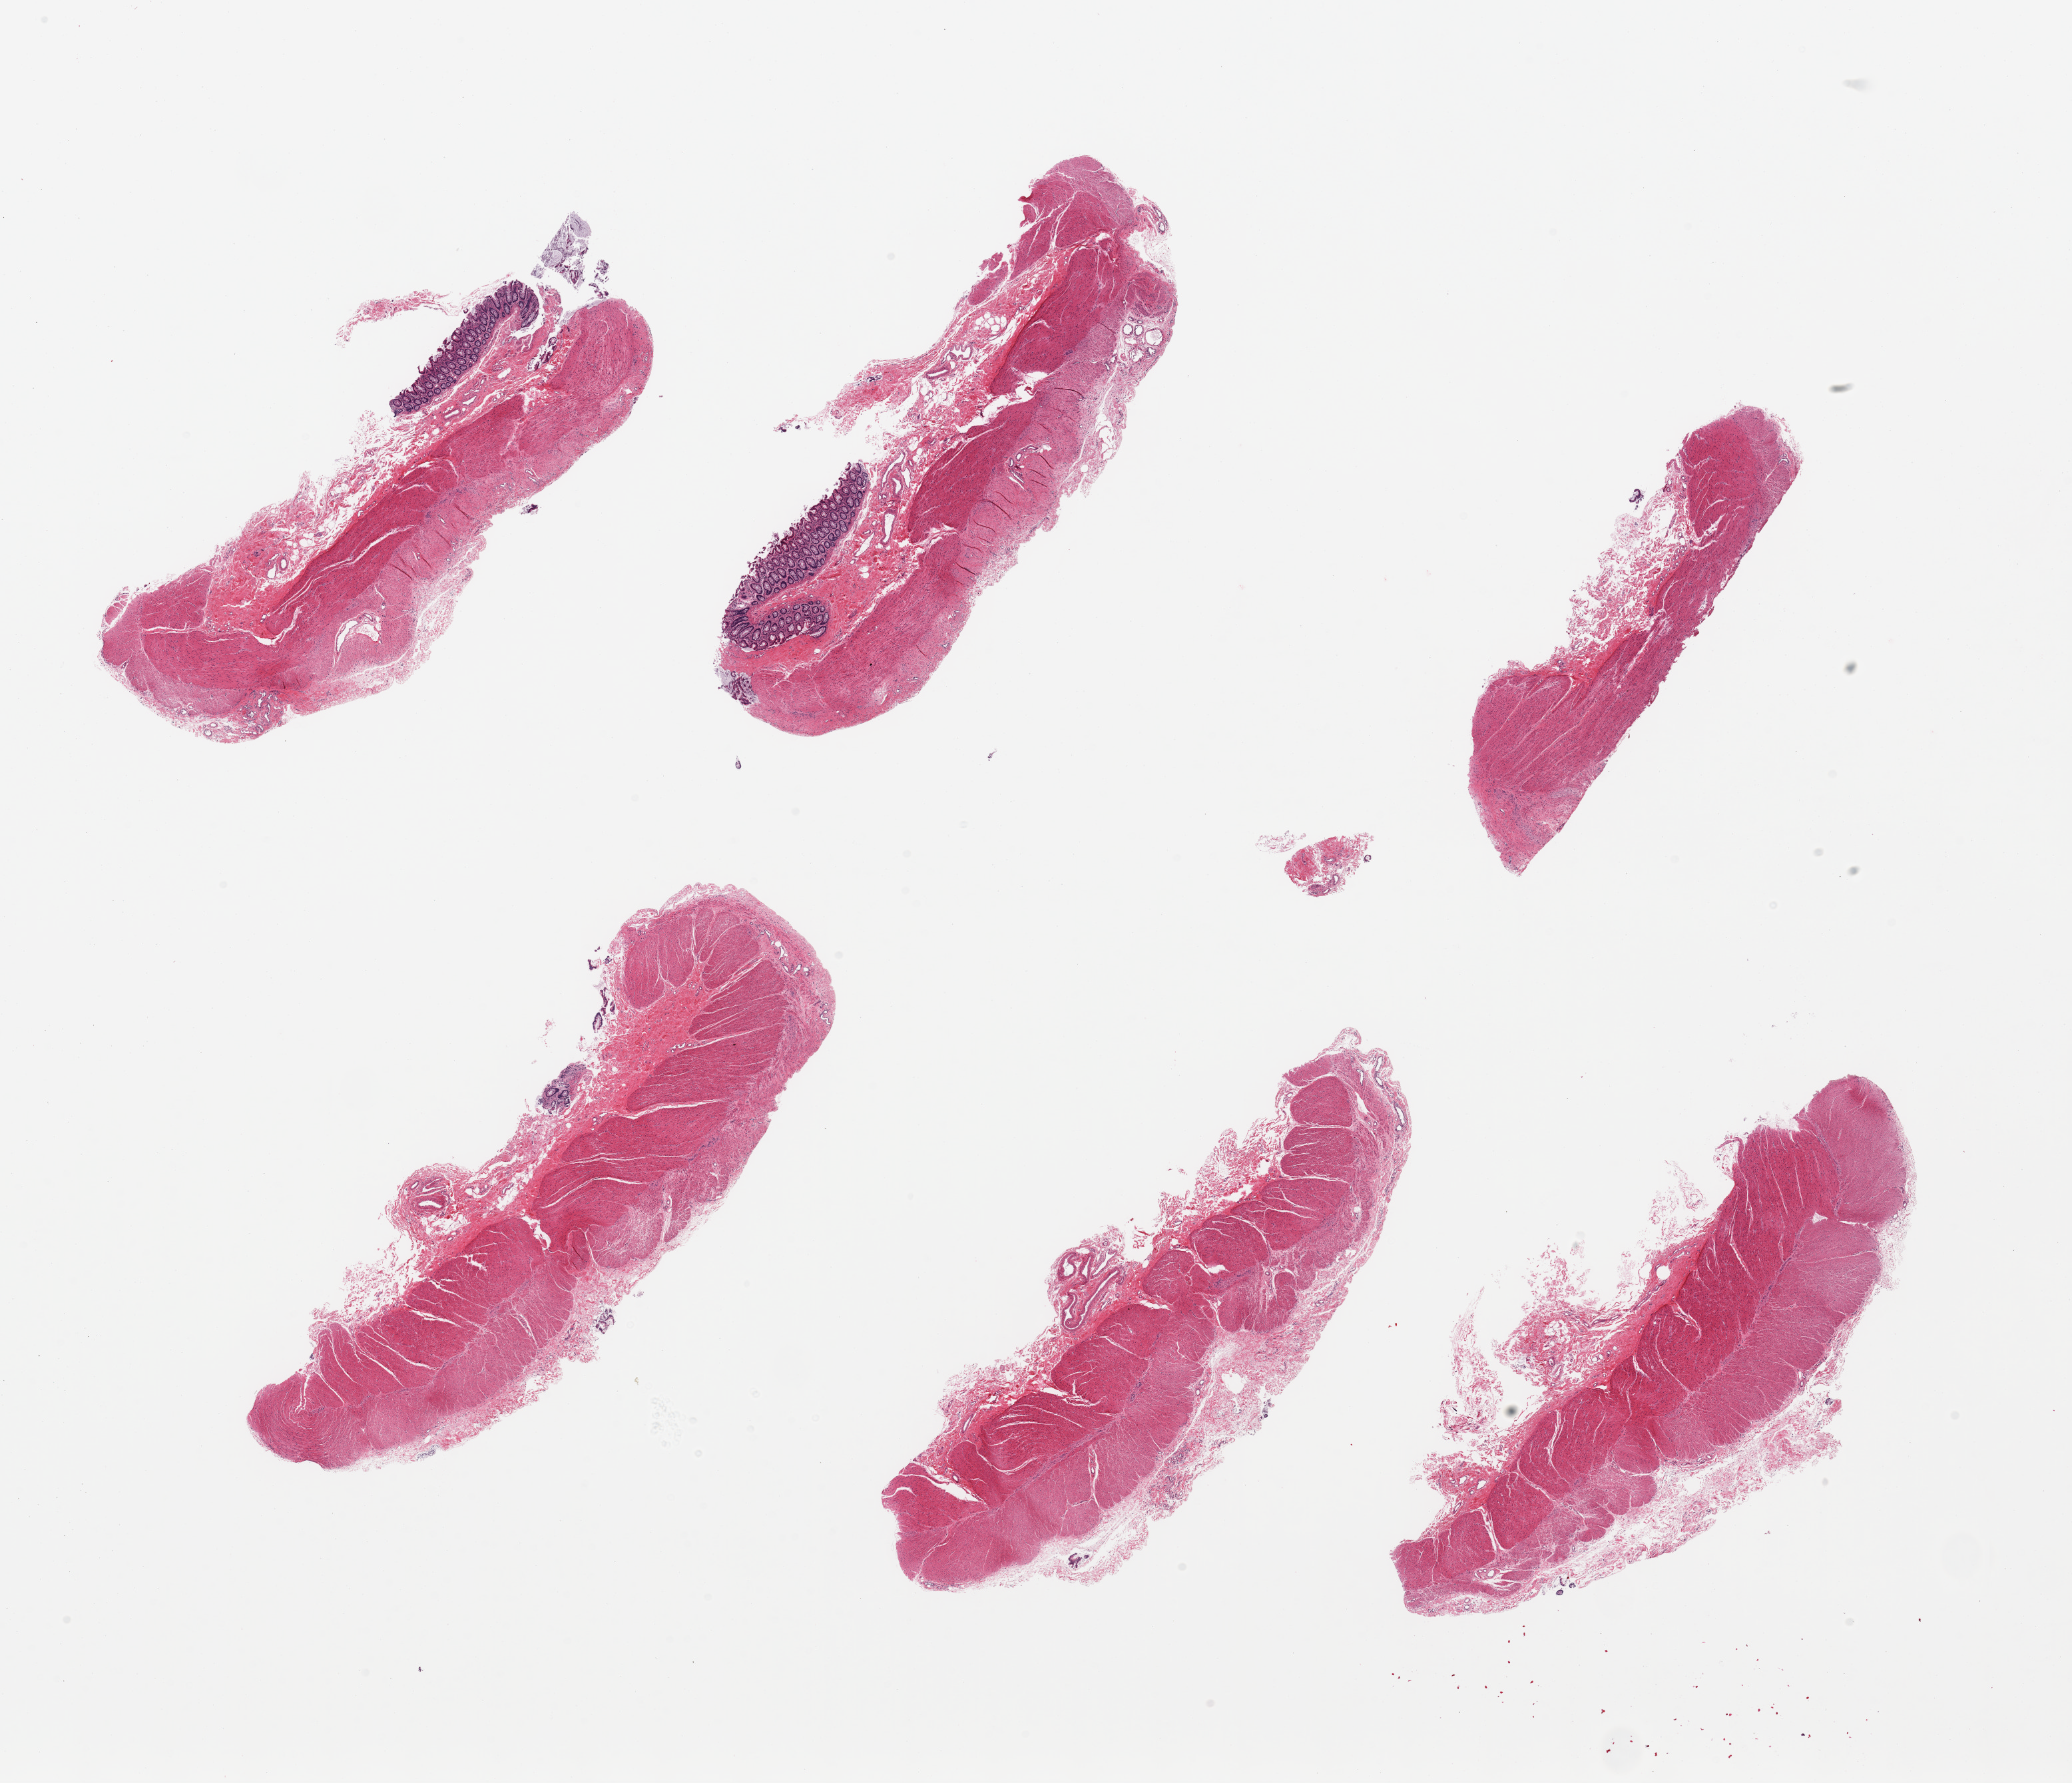
H&E whole-slide image — whole scanned area (about 24.6 x 21.2 mm) shown as a low-resolution overview. PAXgene-fixed paraffin-embedded (PFPE) section. Target tissue: transverse colon. Tissue donor sample. Donor sex: female.
Pathologist's review note for this sample: 6 pieces, mucosa up to ~0.5mm, ~15-20% thickness, much is sloughed/dendued.